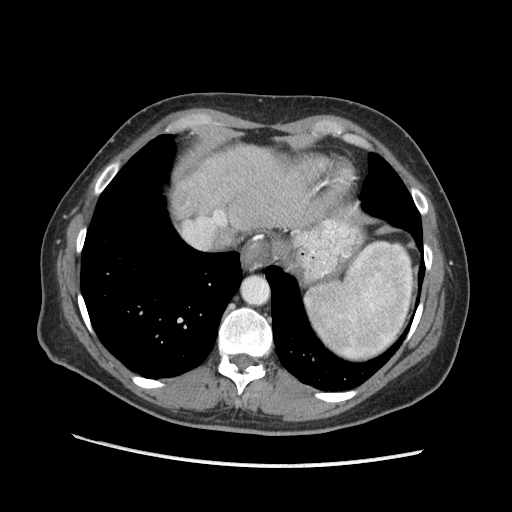
Contrast-enhanced abdominal CT (liver protocol), one axial slice. Position 154 of 170 along the scan axis. 140 kVp. Soft-tissue window (W 400 / L 40 HU). 2.5 mm slice thickness. 512 × 512 image matrix, field of view 360 × 360 mm. Case-level facts recorded for this patient, not image findings: diagnosis: hepatocellular carcinoma (patient treated with transarterial chemoembolisation; whether this scan precedes or follows treatment is not stated here); TNM stage (as recorded): Stage-II.
Annotated regions visible in this slice (semi-automatic segmentation, software-assisted and operator-edited):
- abdominal aorta: box from (x=242, y=277) to (x=268, y=303) px
- liver parenchyma outside the tumour (the mass and vessels are separate outlines, so this box may not span the whole liver): (x=172, y=144)–(x=318, y=230)
- liver vessels: (x=215, y=211)–(x=223, y=214)